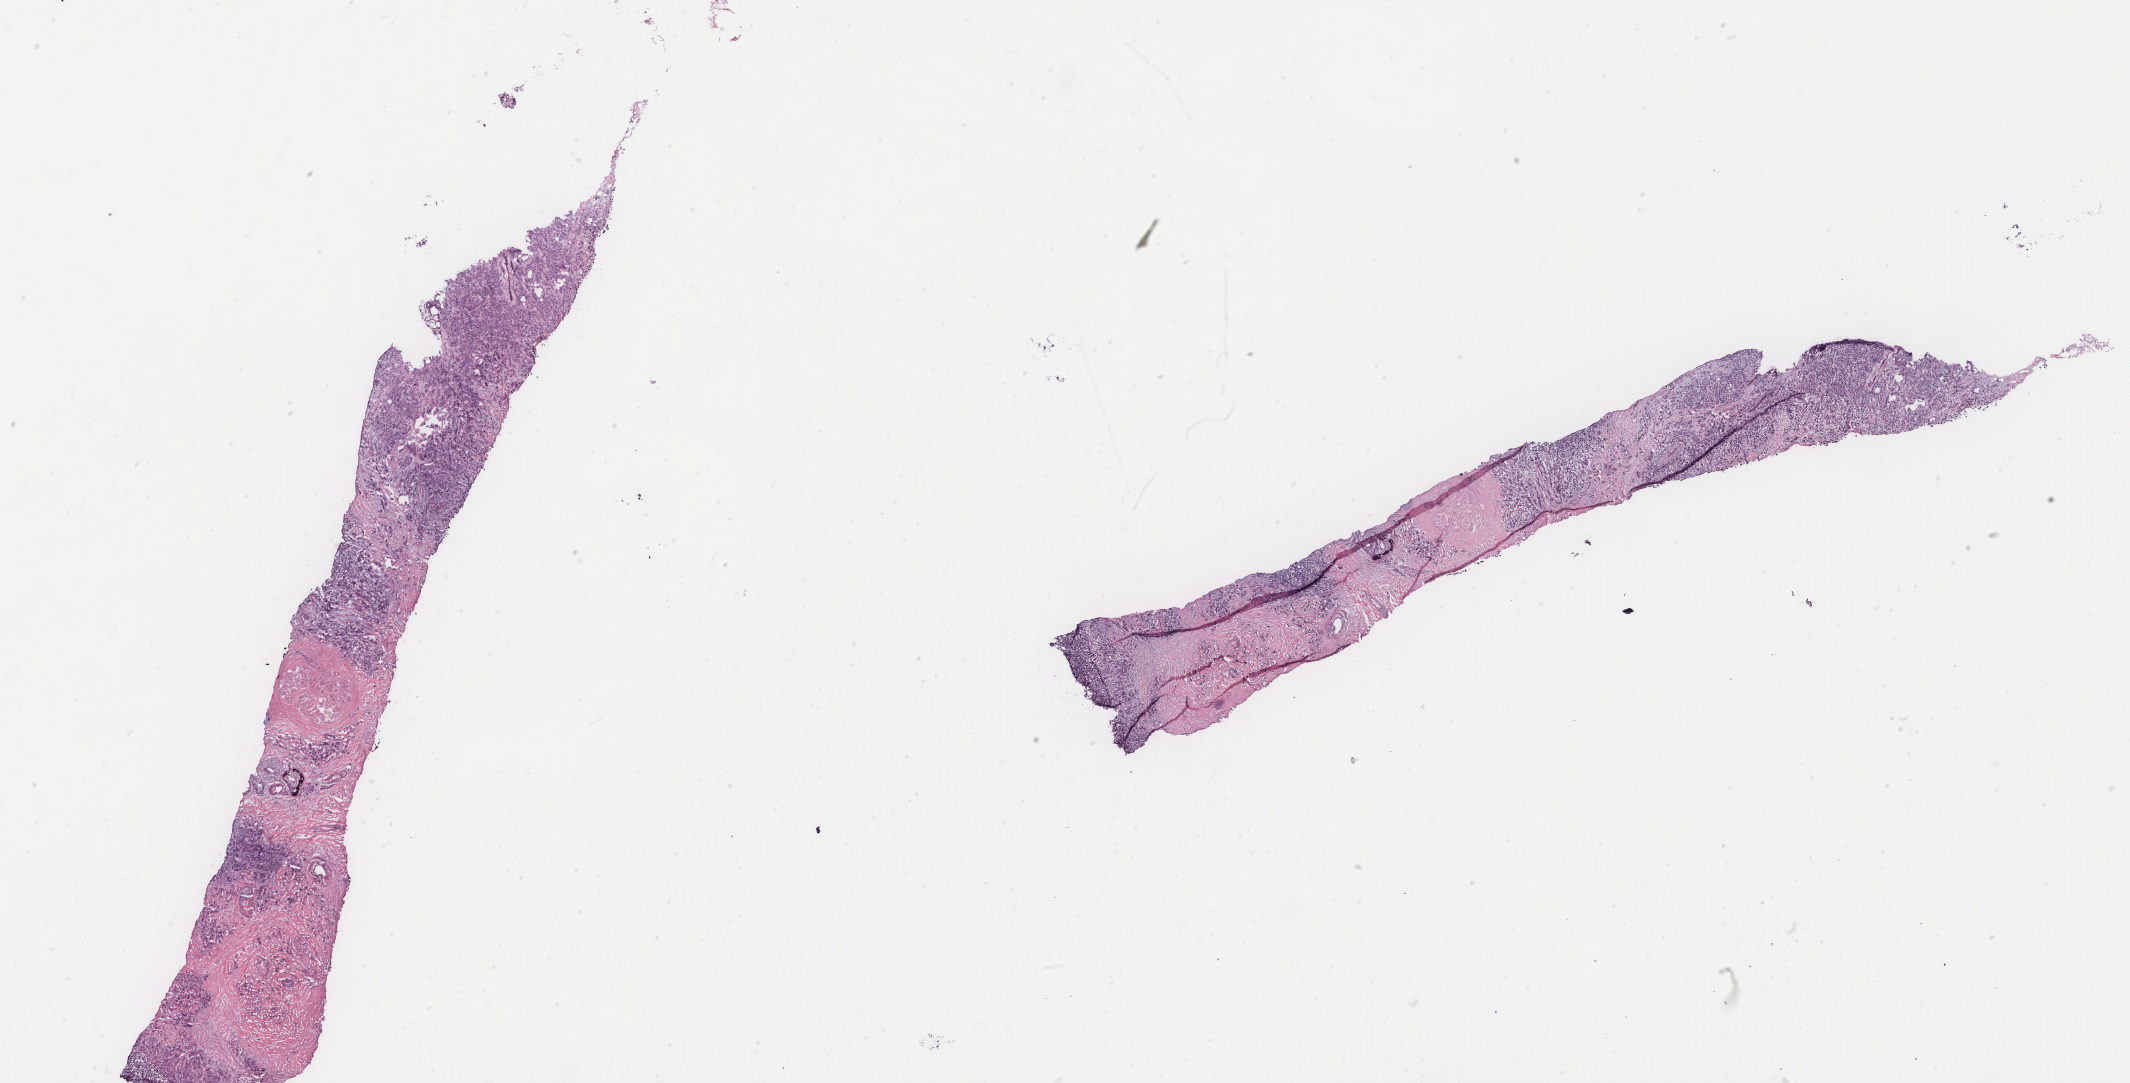
H&E-stained whole-slide image, whole scanned area (about 34.1 x 17.3 mm, acquisition: 40x scan) shown as a low-resolution overview; tumour tissue sample, breast. 88-year-old female patient.
Diagnosis: Infiltrating duct carcinoma, NOS. AJCC pathologic stage: IIB.